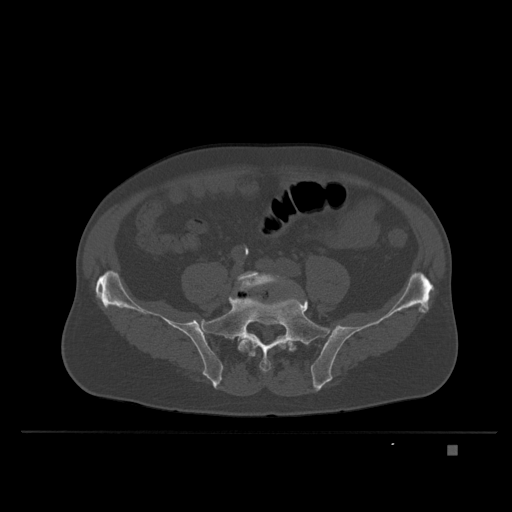
CT including the spine, one axial slice. Slice 44 of 435 in the series (ordered by position). Bone window (W 1800 / L 400 HU). 1.5 mm slice thickness. 512 × 512 image matrix. Male patient, age 73 years. From the clinical record (not read from this slice): primary cancer: skin.
Outlined on this slice (semi-automatically segmented with operator editing):
- L5 vertebra: bounding box <236,271,296,357> (left, top, right, bottom; pixels)